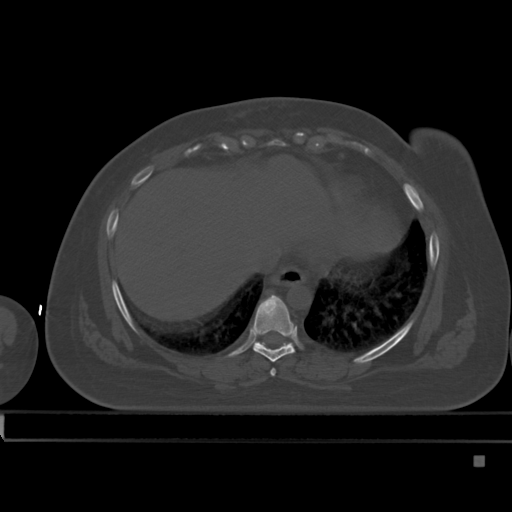
CT including the spine, one axial slice; position 274 of 495 along the scan axis; bone window (W 1800 / L 400 HU); 1.5 mm slice thickness; 512 × 512 image matrix, field of view 404 × 404 mm. Patient: female, 33 years. From the clinical record (not read from this slice): primary cancer: breast; vertebrae with lytic lesions (as recorded): T1.
Annotated regions visible in this slice (semi-automatic segmentation, software-assisted and operator-edited):
- T7 vertebra: bounding box [x1, y1, x2, y2] px = [270, 368, 276, 376]
- T8 vertebra: [252, 295, 295, 362]
- T9 vertebra: [253, 340, 289, 347]